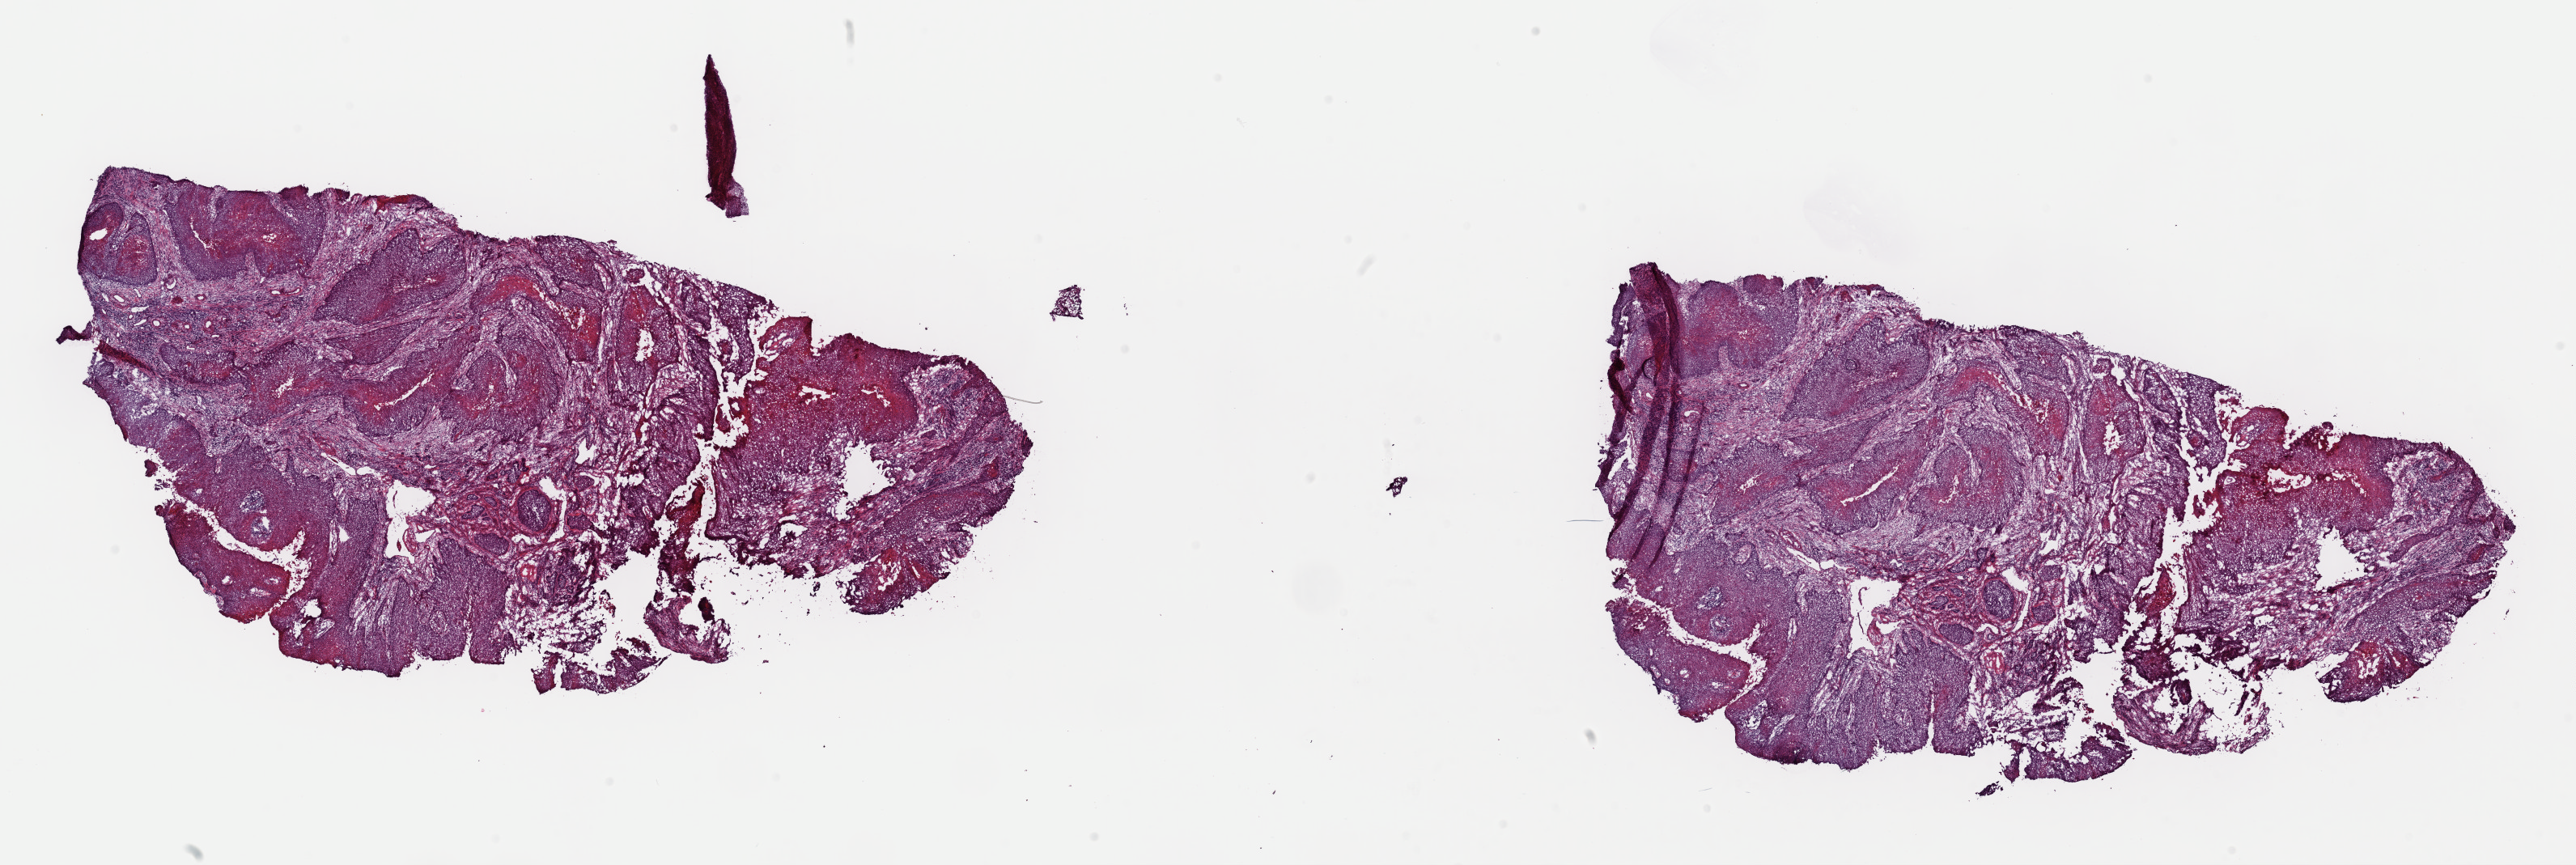
Hematoxylin and eosin (H&E) stained whole-slide image, a low-resolution overview of the entire scanned area, about 25.1 x 8.4 mm (from a 40x scan), frozen section from the top of the tissue portion, primary tumour sample from the cervix. Patient: female, age at initial diagnosis 76 years. Histologic grade: G2 (moderately differentiated). Slide review estimates, as recorded: tumour cells 85%, tumour nuclei 75%, normal cells 0%, stromal cells 15%, necrosis 0%. Infiltration values recorded for this section: lymphocyte infiltration 0%, monocyte infiltration 0%, neutrophil infiltration 0%.
- FIGO stage: IB2
- diagnosis: Squamous cell carcinoma, keratinizing, NOS